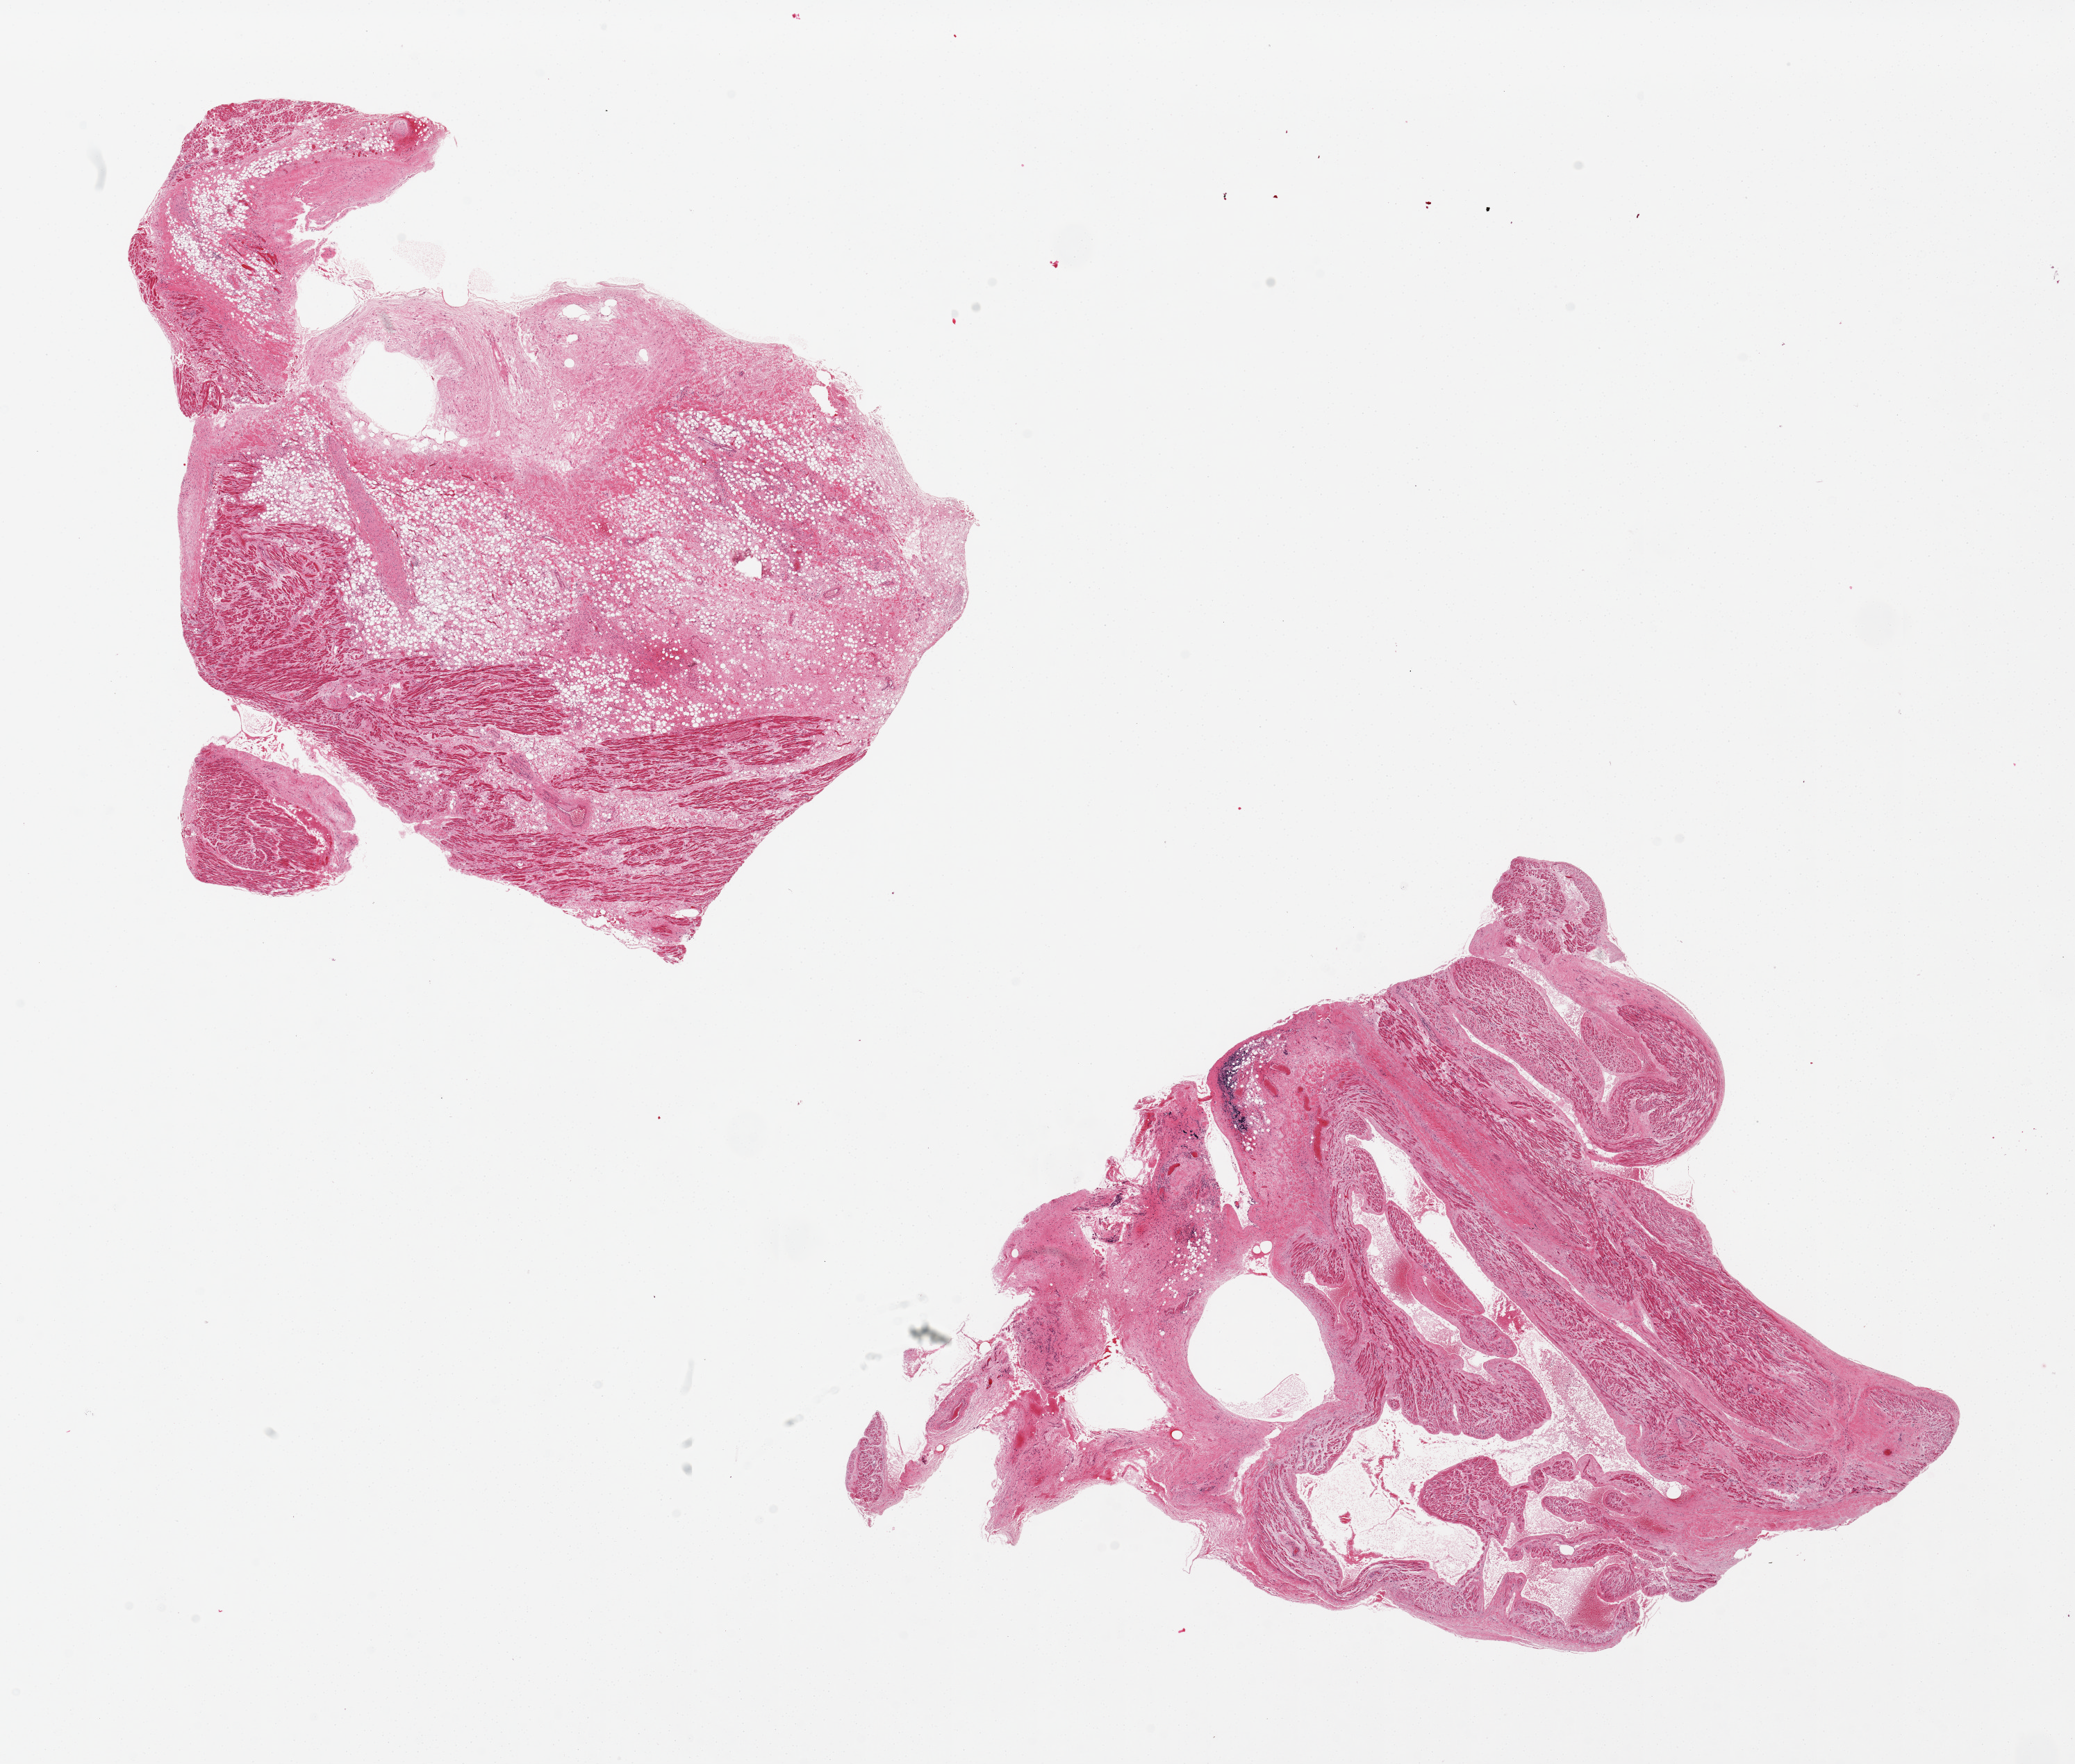
Digitized H&E-stained section — low-resolution overview of the scanned area, about 23.6 x 20.1 mm (slide scanned at 20x), PAXgene-fixed, paraffin-embedded tissue, sampled site (target tissue): auricular appendage, donor tissue sample. Donor: male.
Review note (as recorded): 2 pieces, one with ~40% fat; patchy and interstitial fibrosis.